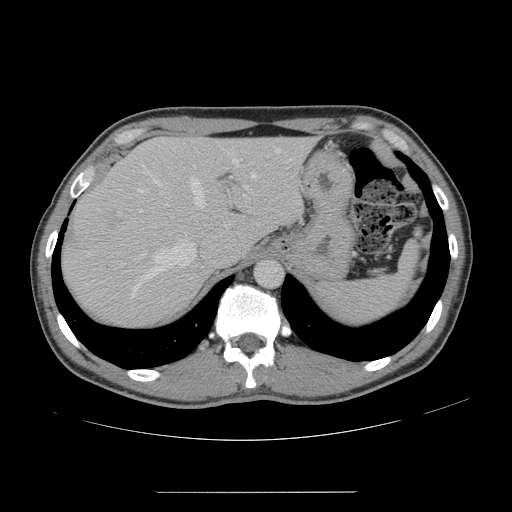
Contrast-enhanced abdominal CT, one axial slice; position 116 of 178 along the scan axis; 120 kVp; intravenous contrast given; soft-tissue window (W 400 / L 40 HU); 2.5 mm slice thickness; 512 × 512 image matrix. Male patient, age 53 years. Case-level facts recorded for this patient, not image findings: diagnosis: colorectal cancer liver metastases, imaged before liver resection; multiple liver metastases: yes; largest metastasis: 2.4 cm; disease in both lobes: no.
Outlined on this slice (outlined manually by an expert reader):
- hepatic veins: bounding box <132,148,280,296> (left, top, right, bottom; pixels)
- liver: <64,138,310,325>
- planned liver remnant (the part of the liver to remain after resection): <147,137,310,247>
- portal vein (with intrahepatic branches): <138,185,250,213>
- liver metastasis: <108,211,120,229>